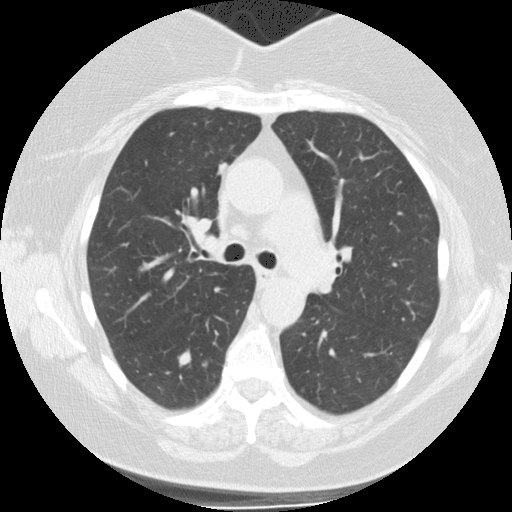
Low-dose screening chest CT, axial slice, baseline screening round, lung window (W 1500 / L -600 HU), 2.5 mm slice thickness, standard (soft-tissue) reconstruction kernel (STANDARD). Female participant, aged 62 years at enrolment. Current smoker at enrolment.
- Expert-annotated lung lesion, bounding box (x1, y1, x2, y2) in pixels: (201, 153, 240, 189).
- The screening reader recorded 3 non-calcified nodules or masses ≥4 mm on this exam; which of them this box marks is not recorded.
- Official screen result: positive, change unspecified: nodule(s) >= 4 mm or enlarging nodule(s), mass(es), or other non-specific abnormalities suspicious for lung cancer.
- Later outcome: lung cancer diagnosed 929 days after this screen (after the third annual screen) — adenocarcinoma, NOS, right upper lobe, poorly differentiated (G3), stage IB (AJCC 6th edition), 12 mm at pathology.